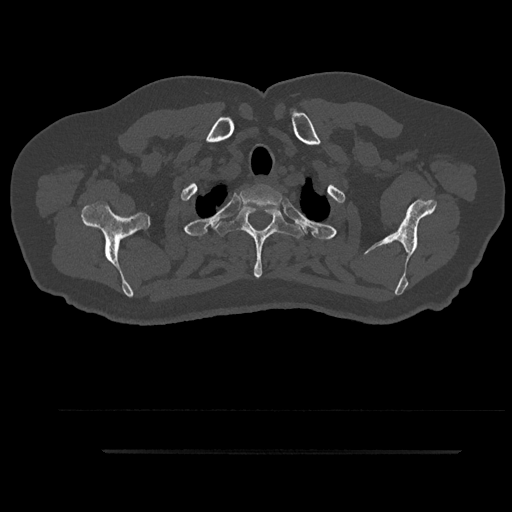
CT including the spine, one axial slice; position 768 of 797 along the scan axis; reconstruction kernel Br40s/3; 120 kVp; bone window (W 1800 / L 400 HU); 0.5 mm slice thickness; 512 × 512 image matrix. Male patient, age 63 years. From the clinical record (not read from this slice): primary cancer: renal.
Structures marked on this image (semi-automatic segmentation, software-assisted and operator-edited):
- T1 vertebra: bounding box [x1, y1, x2, y2] px = [239, 185, 282, 222]
- T2 vertebra: [214, 205, 304, 278]